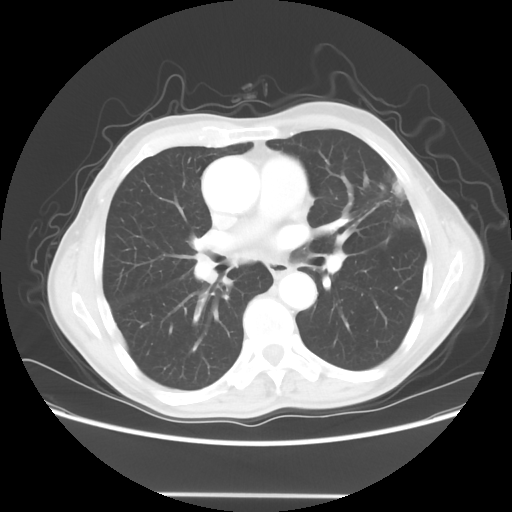
Chest CT, one axial slice. Reconstruction kernel STANDARD. 120 kVp. Lung window (W 1500 / L -600 HU). 5 mm slice thickness. 512 × 512 image matrix. Patient: male, 71 years. Case-level facts recorded for this patient, not image findings: clinical TNM (as recorded): T1c N0 M0; histopathological grade: G2-3.
Structures marked on this image (rectangle marked by the reading radiologist):
- lung tumour (recorded histology: adenocarcinoma): bounding box <382,169,407,203> (left, top, right, bottom; pixels)